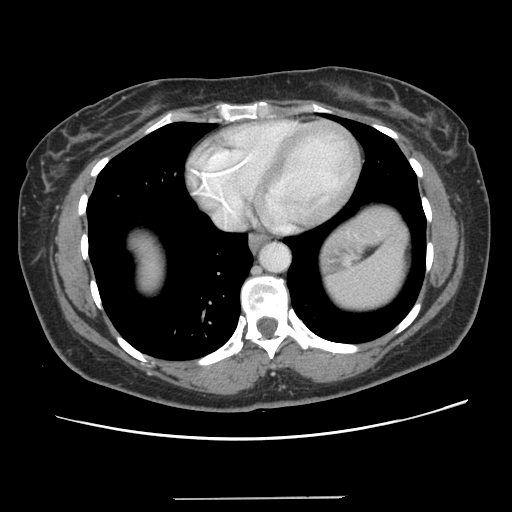
Contrast-enhanced abdominal CT, one axial slice. Position 127 of 141 along the scan axis. Intravenous contrast given. Soft-tissue window (W 400 / L 40 HU). 2.5 mm slice thickness. 512 × 512 image matrix. Female patient, age 53 years. Case-level facts recorded for this patient, not image findings: diagnosis: colorectal cancer liver metastases, imaged before liver resection; multiple liver metastases: no; largest metastasis: 14.5 cm; disease in both lobes: yes.
Structures marked on this image (manually delineated by an expert):
- liver: bounding box (x1, y1, x2, y2) in pixels: (136, 204, 398, 290)
- planned liver remnant (the part of the liver to remain after resection): (137, 245, 163, 288)